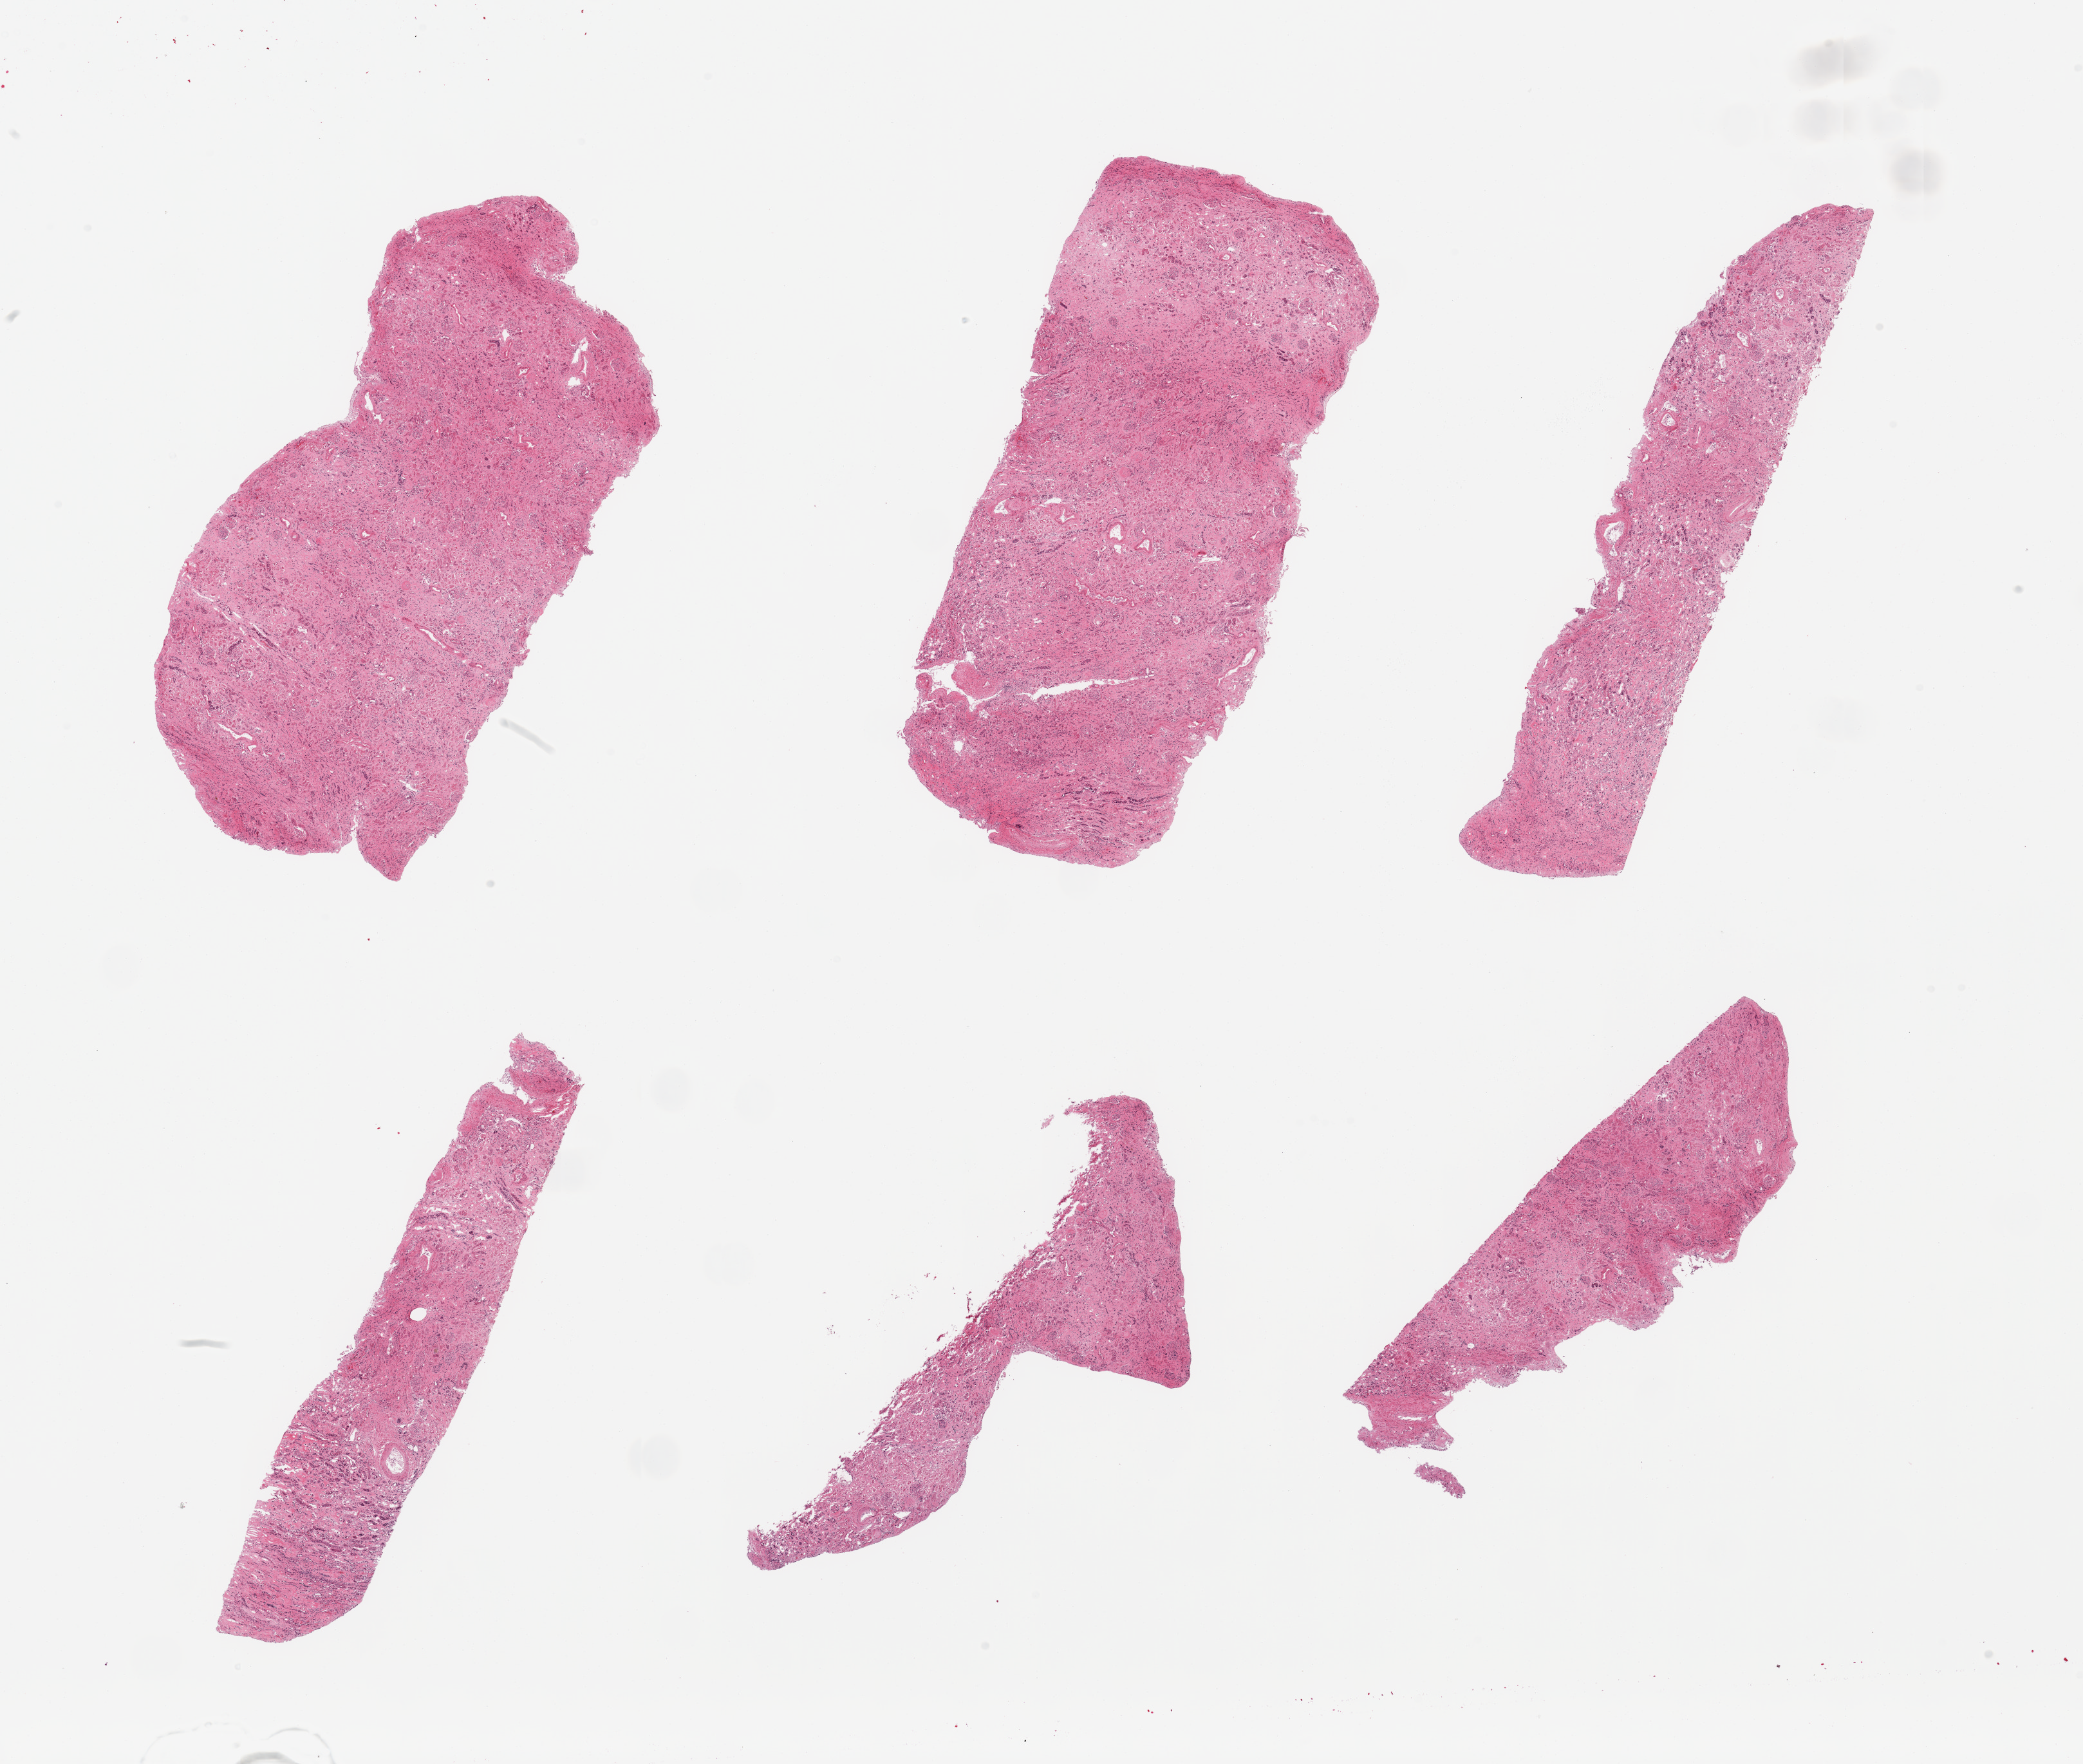
Digitized haematoxylin and eosin-stained section, brightfield — whole scanned area (about 25.6 x 21.7 mm, acquisition: 20x scan) shown as a low-resolution overview; PAXgene-fixed, paraffin-embedded tissue; target tissue: renal cortex; tissue donor sample. Donor sex: male.
Pathologist's review note for this sample: 6 pieces; glomeruli (many hyalinized), present; advanced autolysis.